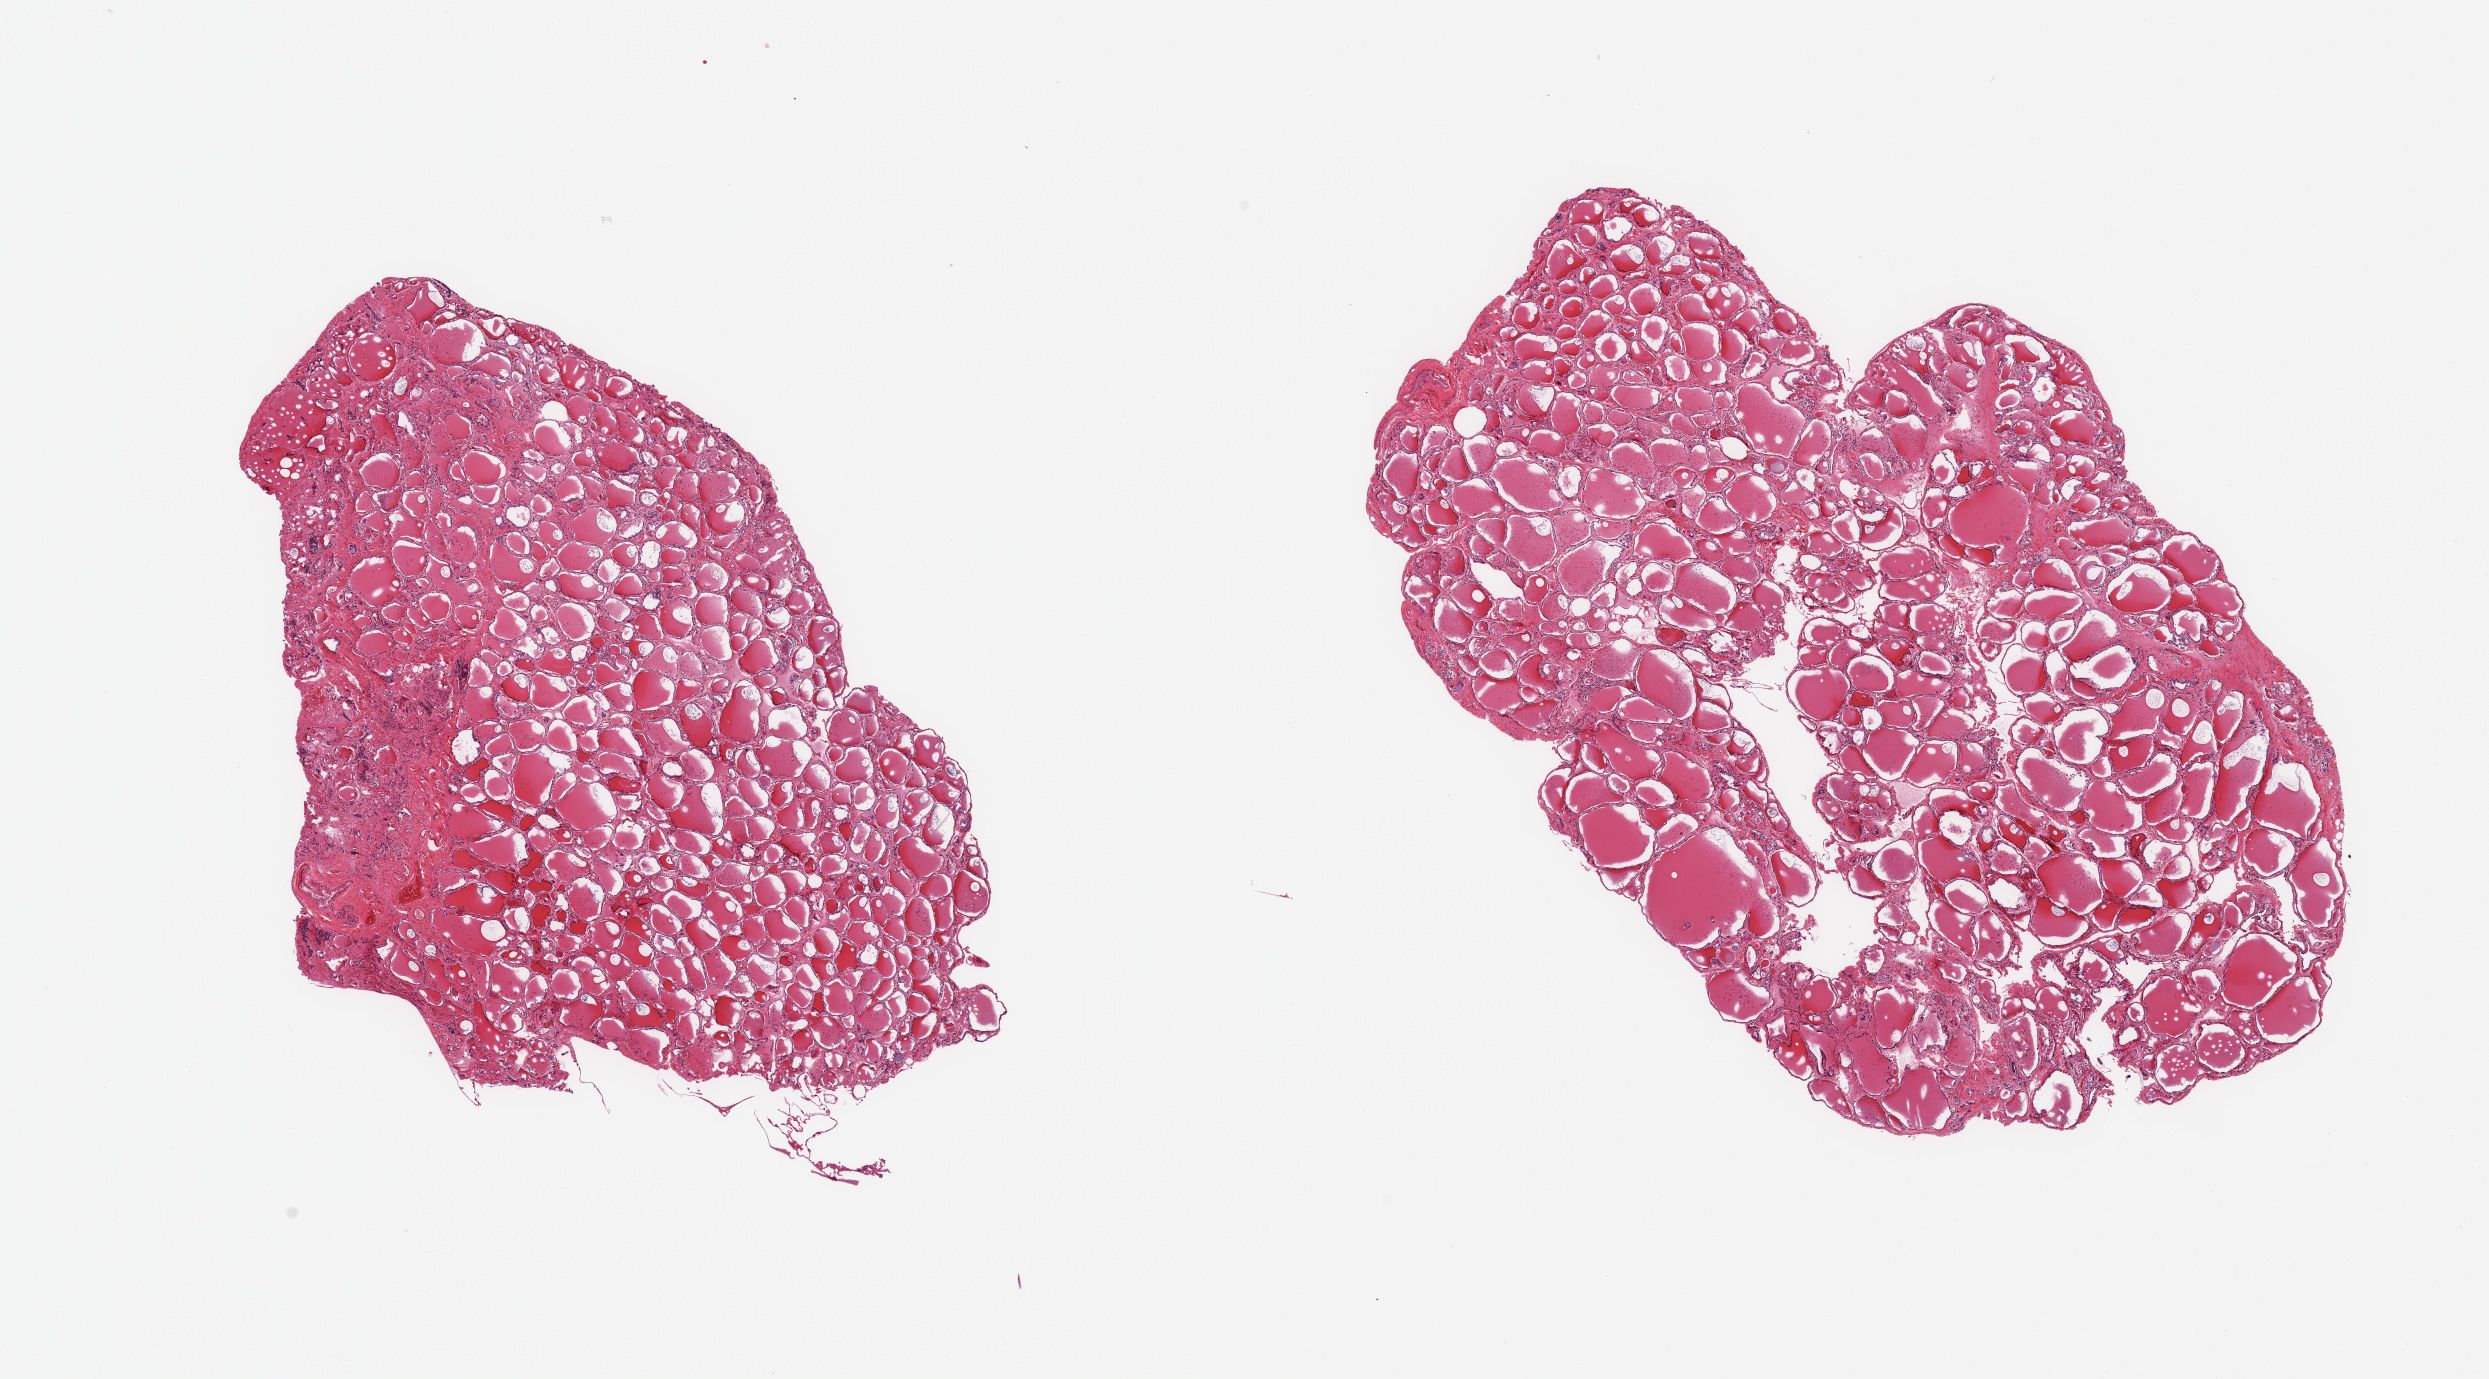
Digitized hematoxylin and eosin (H&E)-stained section, shown as a low-resolution overview of the whole scanned area (about 19.7 x 10.9 mm, acquisition: 20x scan); PAXgene-fixed, paraffin-embedded tissue; sampled site (target tissue): thyroid; donor tissue sample.
• reviewer comment on this tissue sample: 2 pieces, no abnormalities